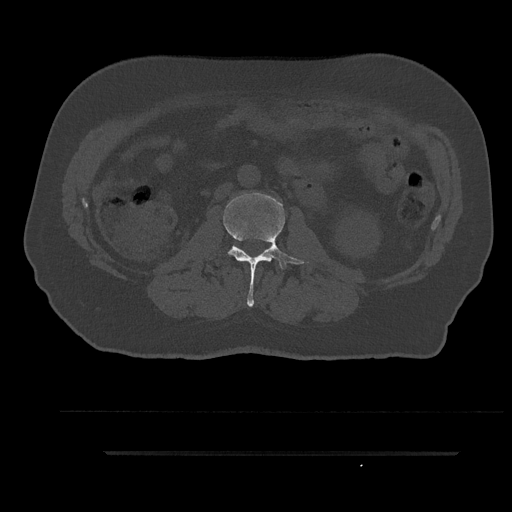
CT including the spine, one axial slice; position 102 of 797 along the scan axis; 120 kVp; bone window (W 1800 / L 400 HU); 0.5 mm slice thickness; 512 × 512 image matrix, field of view 432 × 432 mm. Male patient, age 63 years. Case-level facts recorded for this patient, not image findings: primary cancer: renal; vertebrae with lytic lesions (as recorded): T8.
Structures marked on this image (semi-automatically segmented with operator editing):
- L2 vertebra: bounding box (x1, y1, x2, y2) in pixels: (224, 193, 309, 307)